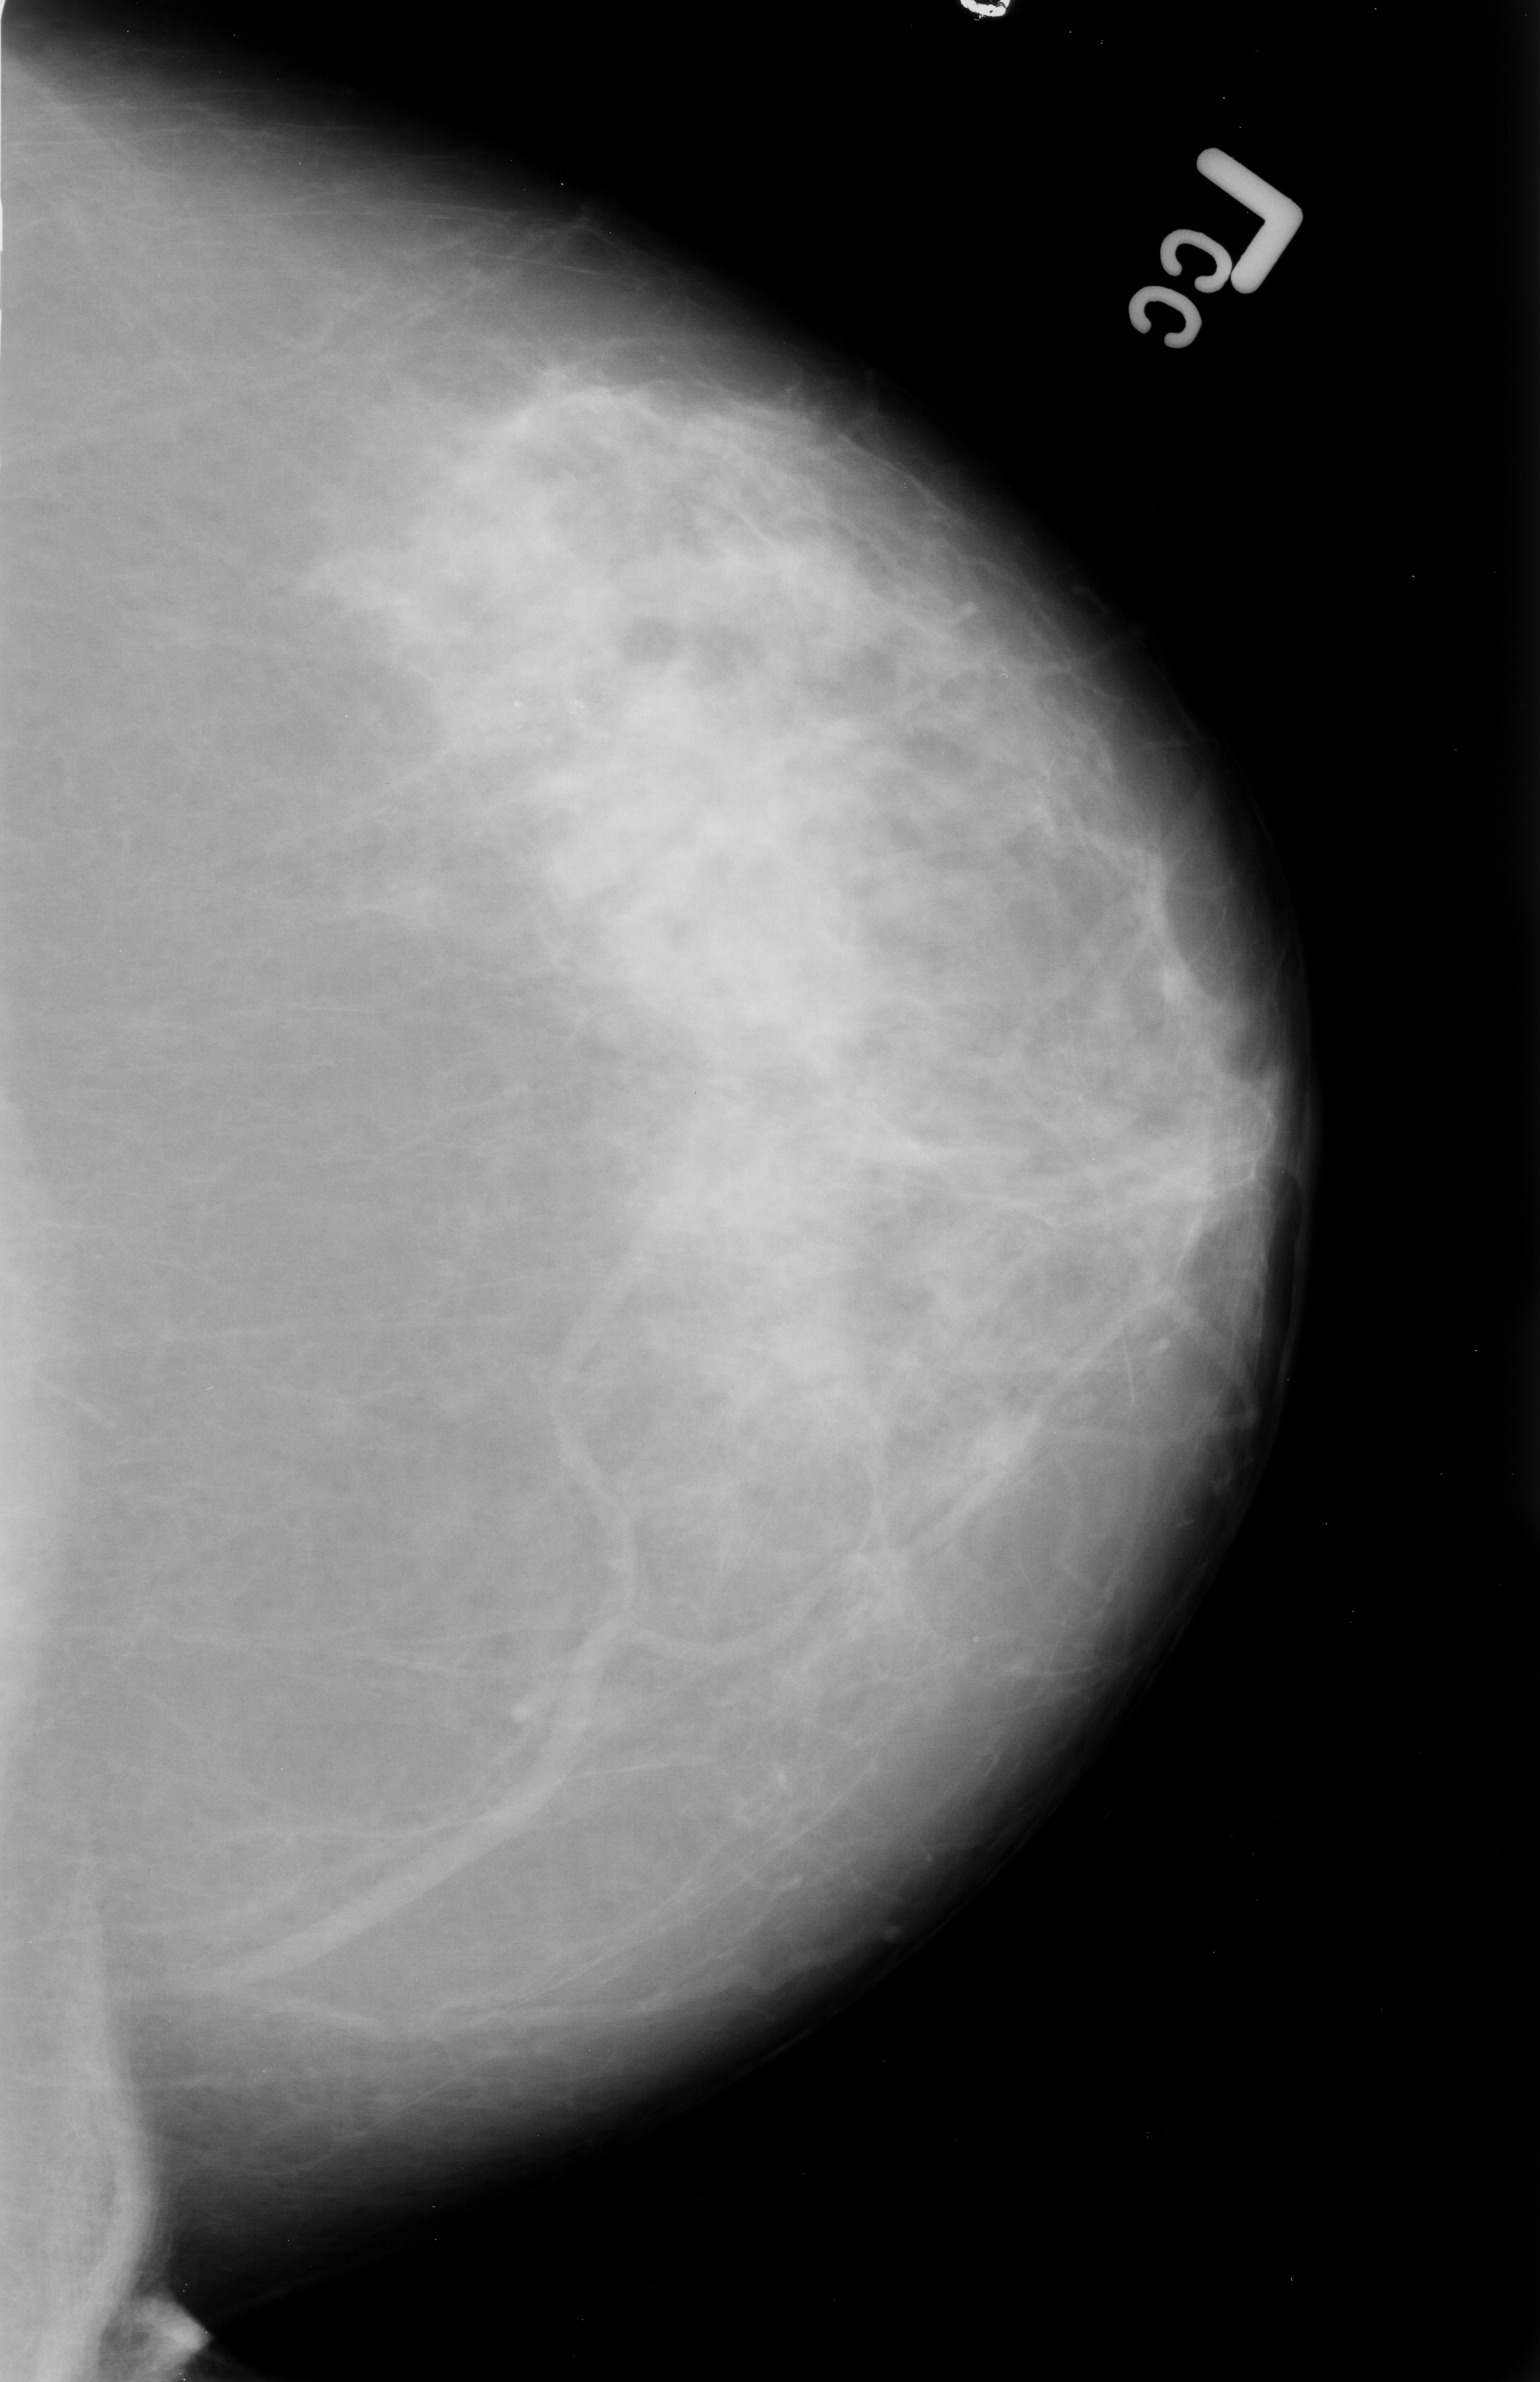
Scanned film-screen mammogram, left breast, craniocaudal (CC) view, BI-RADS breast density category 2 (scale 1–4).
Radiologist-marked abnormalities on this image: calcifications, morphology pleomorphic, distribution clustered; BI-RADS assessment category 4; subtlety rating 3 on a 1 (subtle) to 5 (obvious) scale; pathology result (as recorded, not read from the image): malignant.